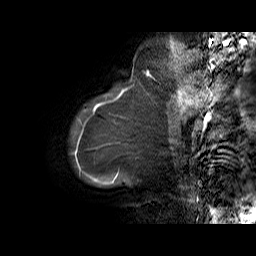
Breast MRI (dynamic contrast-enhanced), one sagittal slice. Slice 4 of 65 in the series (ordered by position). Dynamic contrast-enhanced series, time point 2 of 6 at this slice position (early post-contrast). 1.5 T. TE 5.7 ms, TR 32.9 ms. 4 mm slice thickness. 256 × 256 image matrix, field of view 230 × 230 mm. Female patient. Case-level facts recorded for this patient, not image findings: setting: breast cancer imaged before/during neoadjuvant chemotherapy; receptor status: HER2-positive.
Structures marked on this image (semi-automatic segmentation, software-assisted and operator-edited):
- analysis volume of interest (the breast-tissue region the enhancement analysis was run in; not a lesion): bounding box <86,88,125,111> (left, top, right, bottom; pixels)
- tumour enhancement mask (voxels above the 100 % enhancement threshold inside the analysis volume of interest): <93,90,124,111>